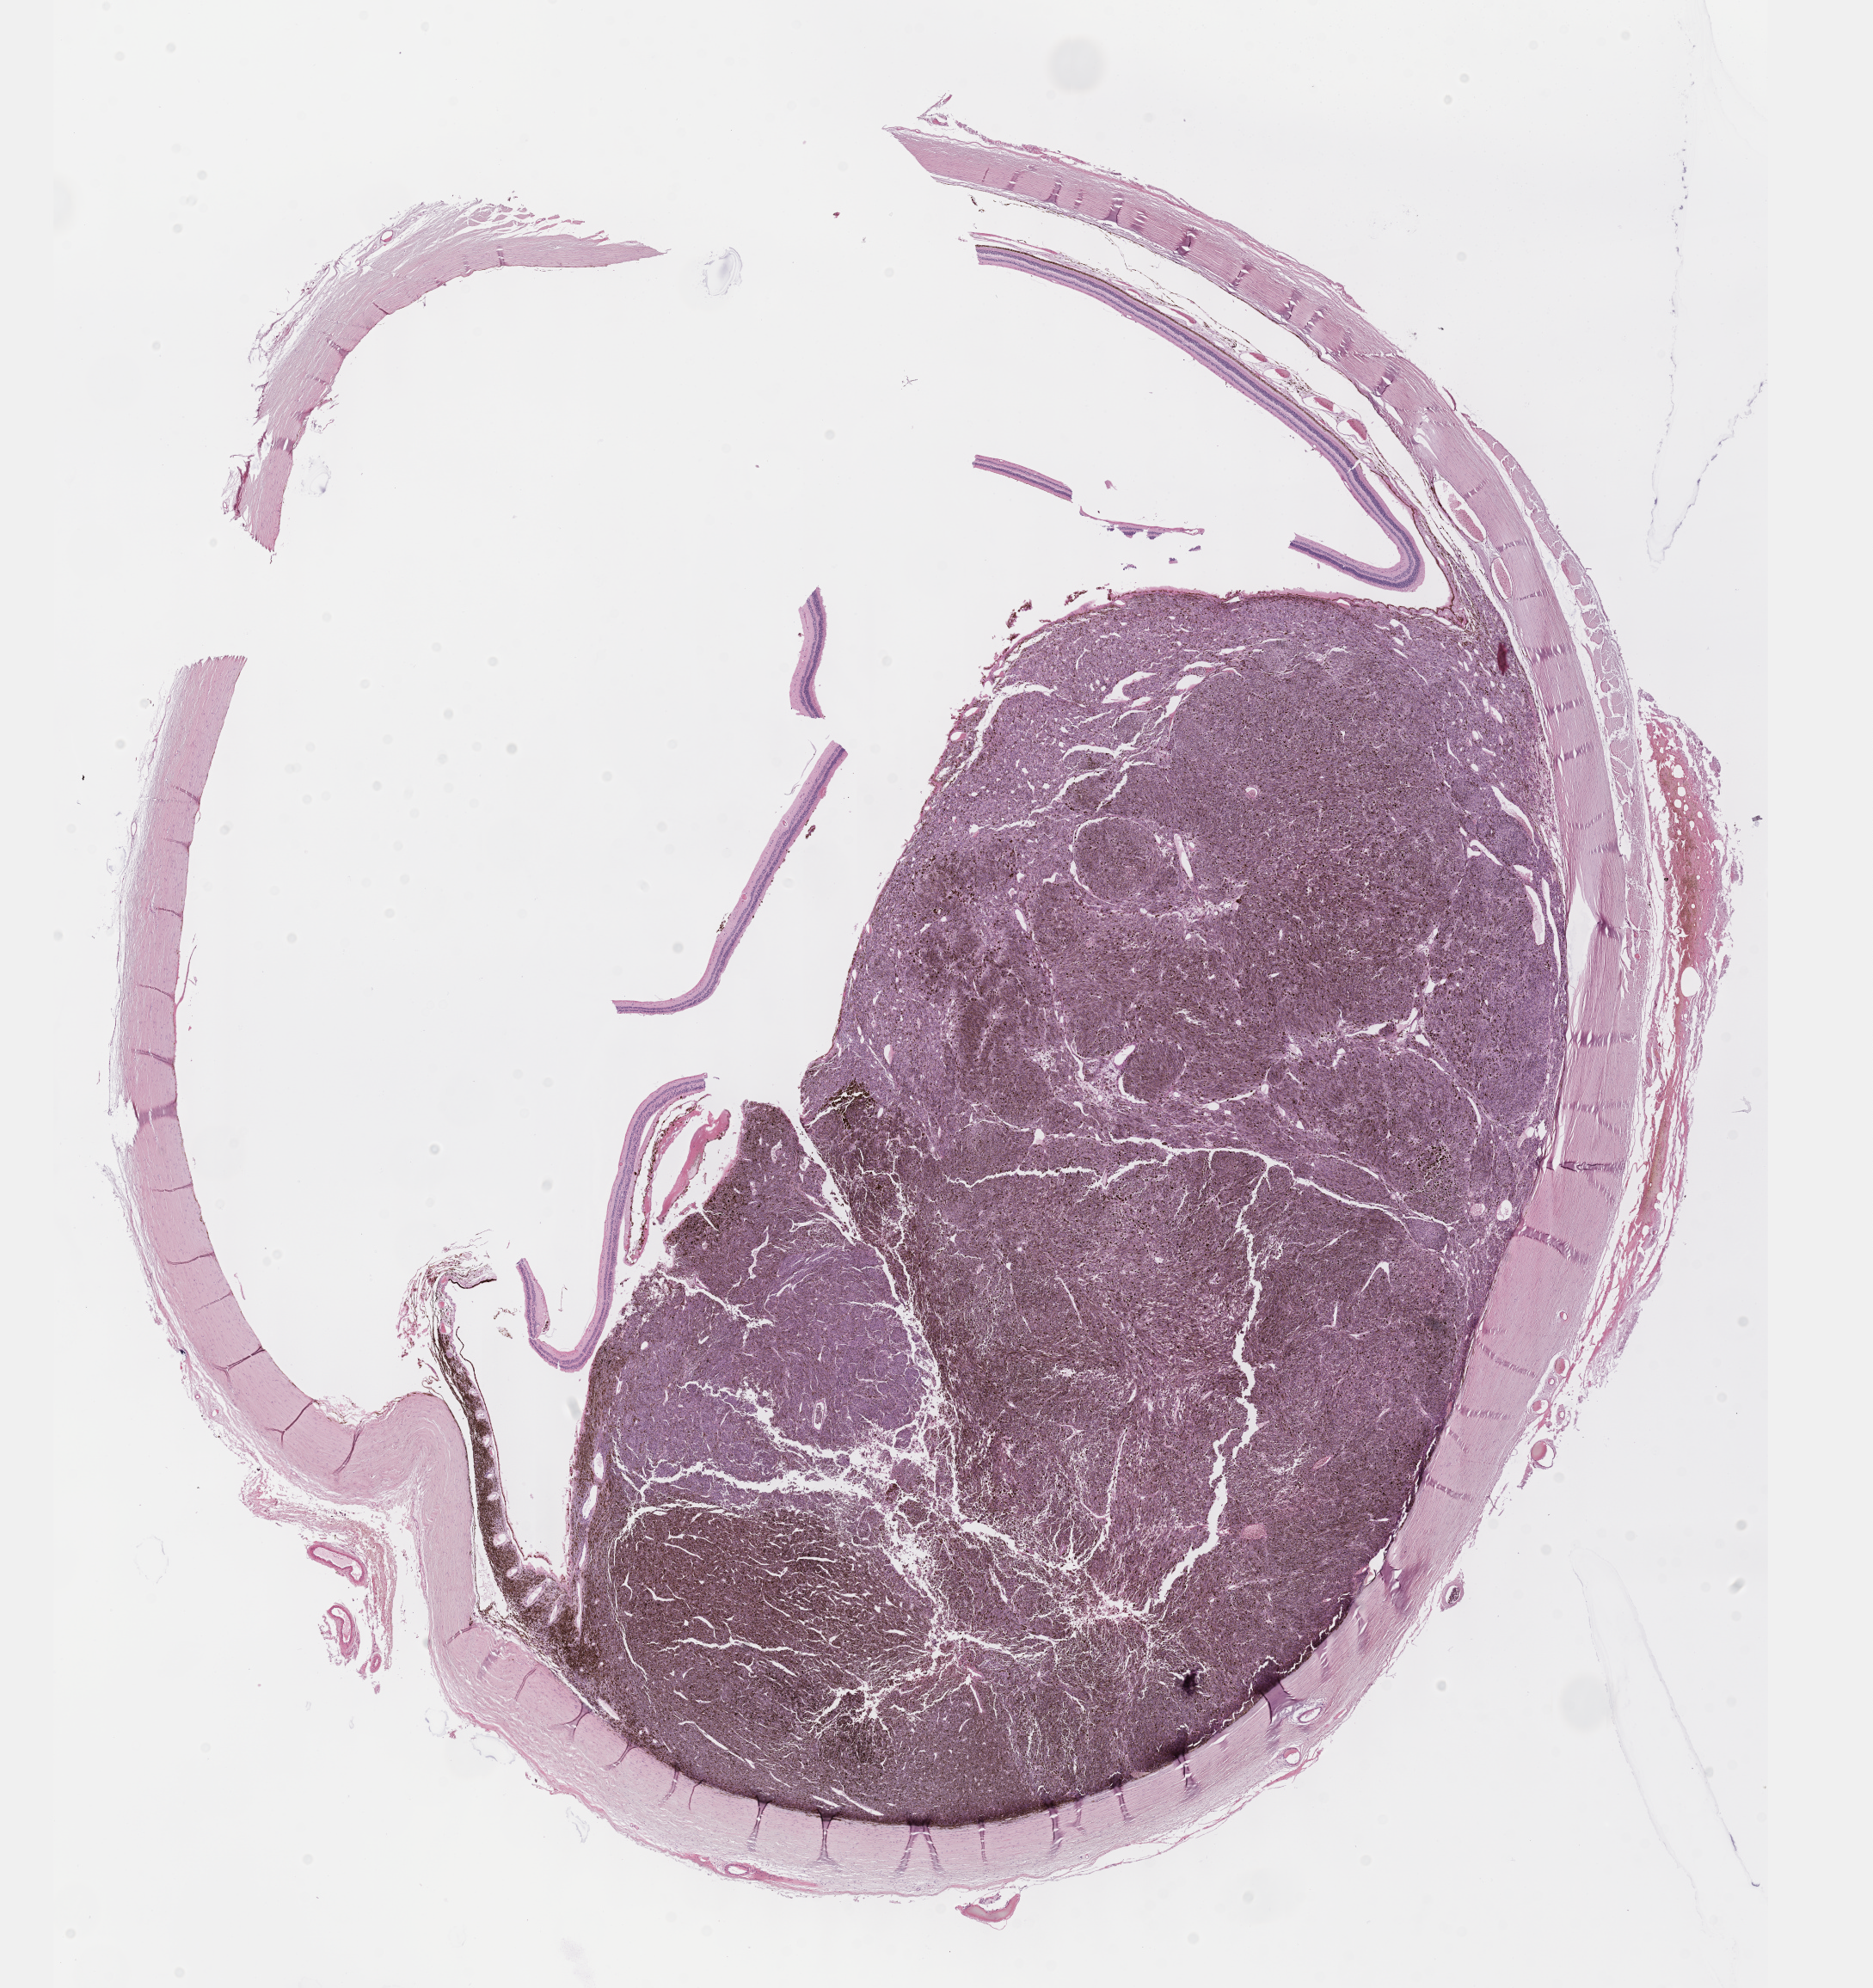
H&E whole-slide image — shown as a low-resolution overview of the whole scanned area (about 17.6 x 18.7 mm); formalin-fixed paraffin-embedded (FFPE) diagnostic section; uvea, primary tumour sample. Male, age 49 years at initial diagnosis.
Pathologic diagnosis: Epithelioid cell melanoma (choroid).